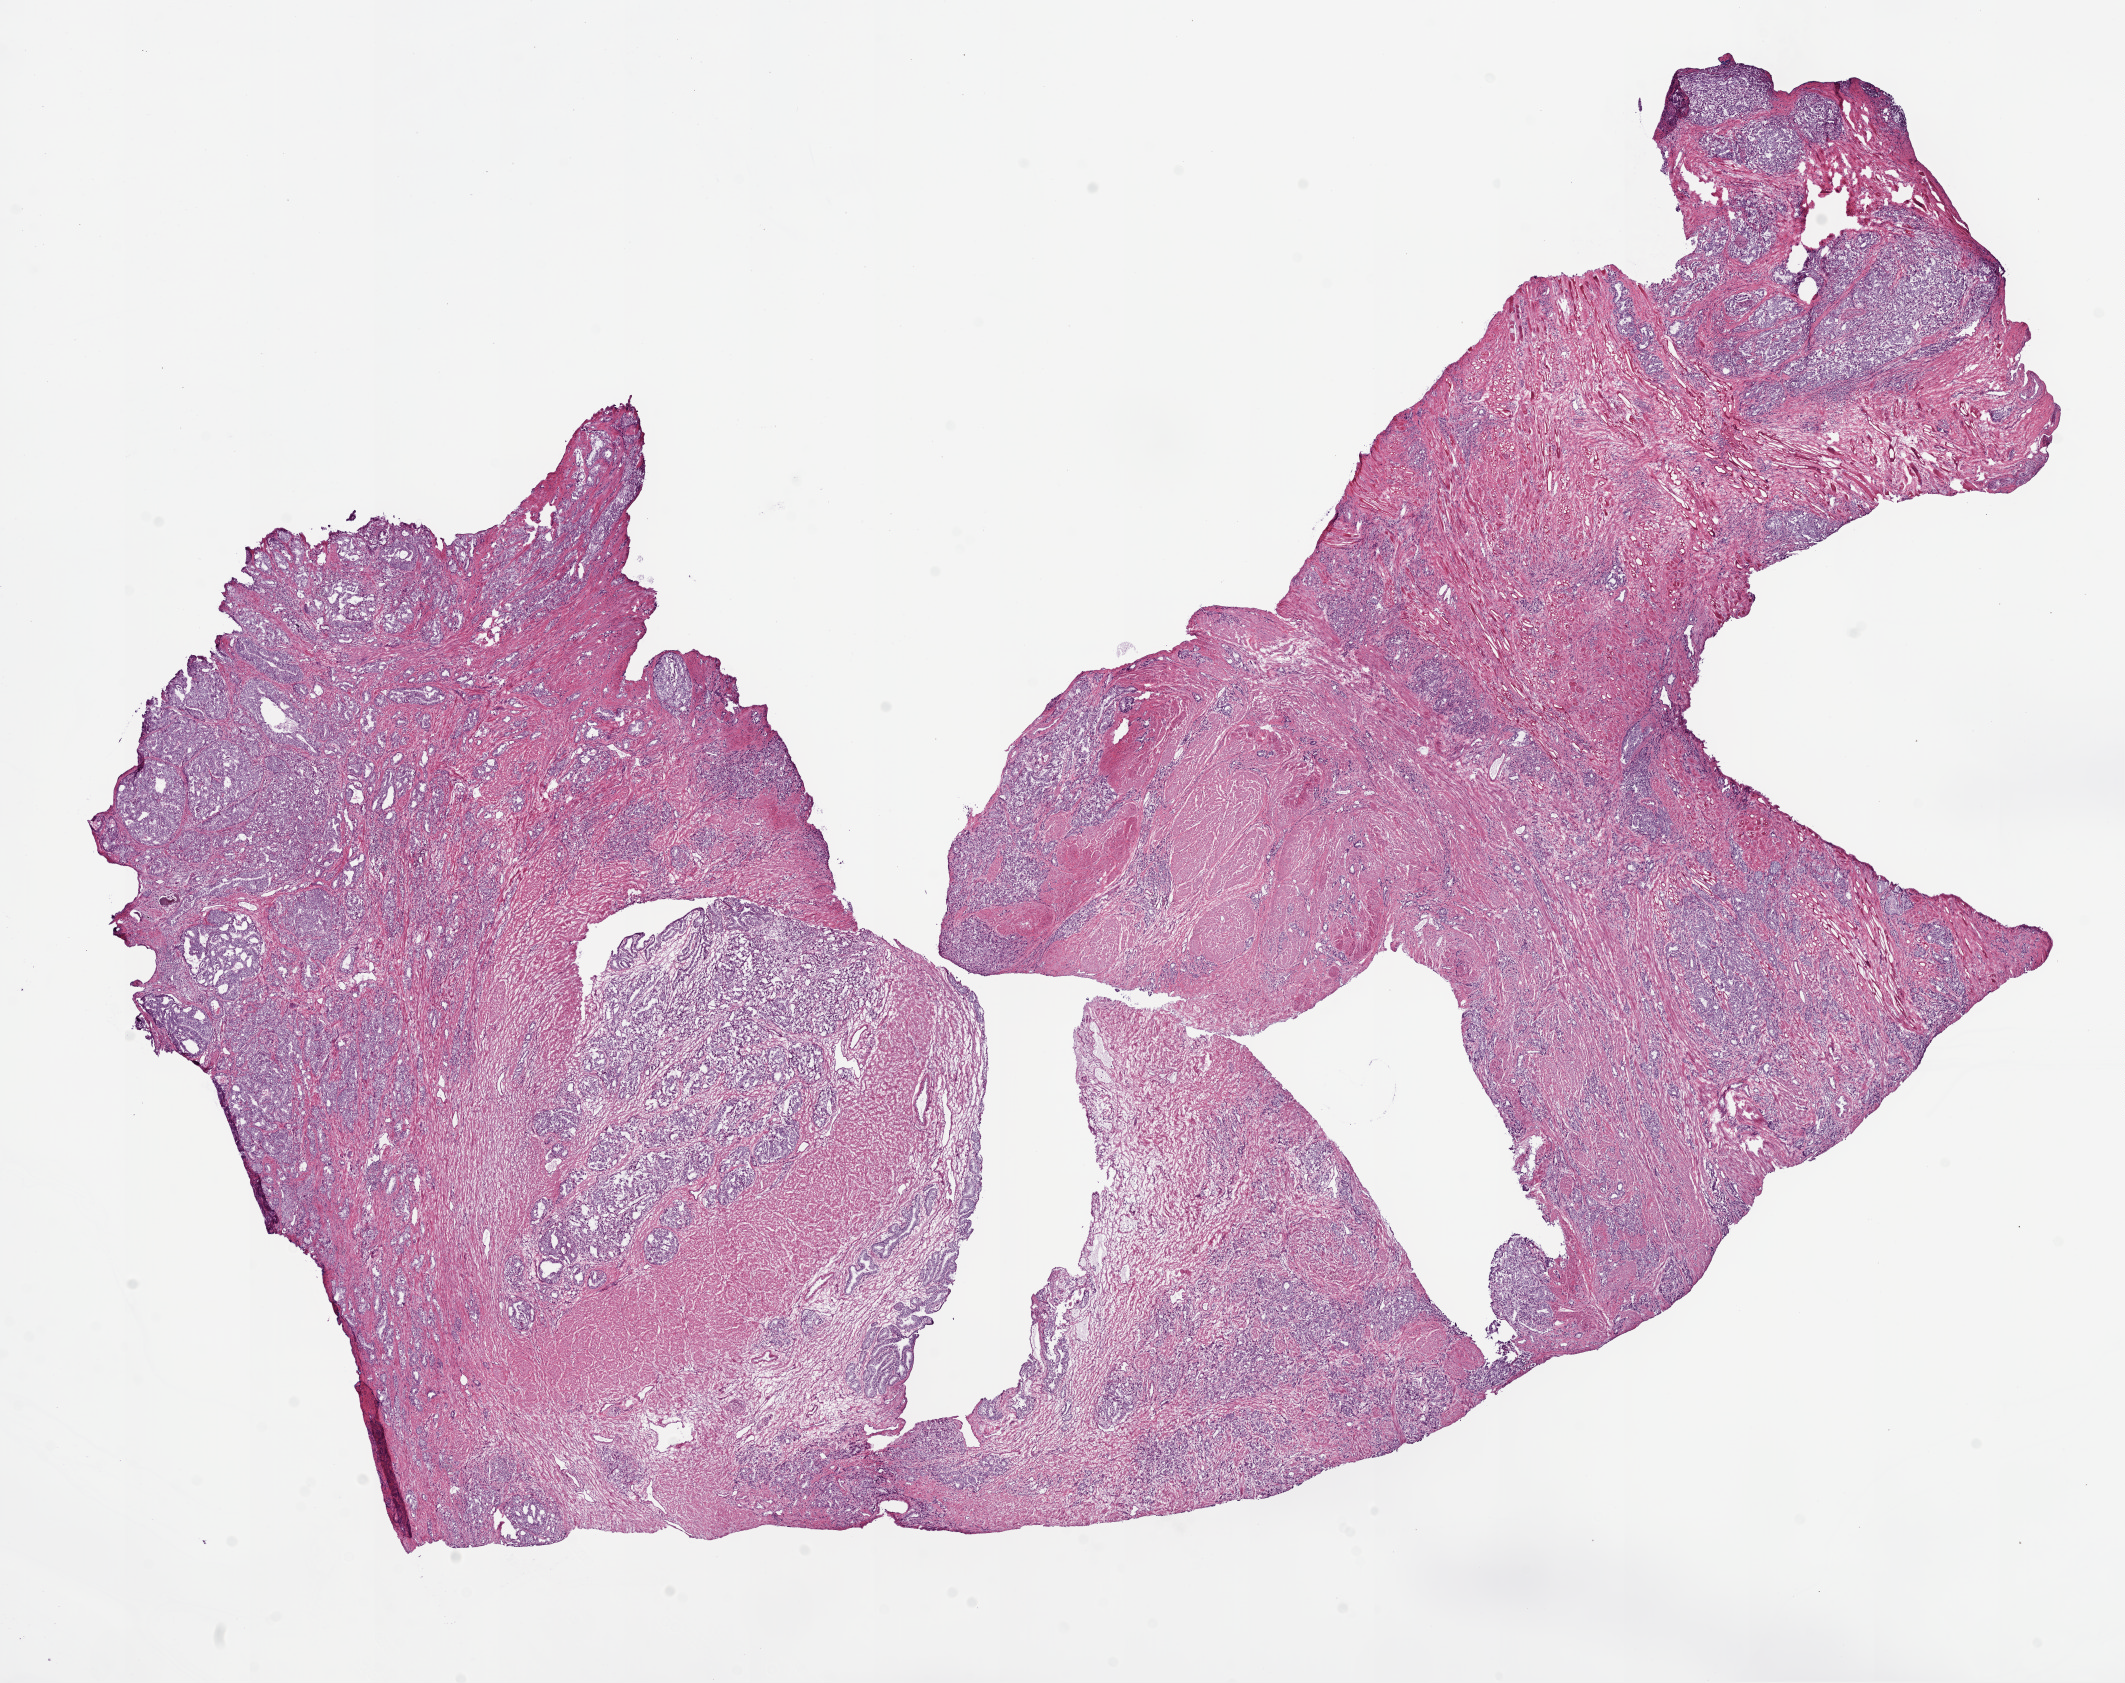
Digitized H&E tissue section (whole slide), shown as a low-resolution overview of the whole scanned area (about 17.1 x 13.5 mm, acquisition: 20x scan); frozen section from the top of the tissue portion; prostate, primary tumour sample. Male patient; age at initial diagnosis 66 years. Gleason score: 9 (4+5). Composition of this section per pathologist review: tumour cells 50%, tumour nuclei 55%, normal cells 20%, stromal cells 30%, necrosis 0%. Infiltration values recorded for this section: lymphocyte infiltration 0%, monocyte infiltration 0%, neutrophil infiltration 0%.
Lymph nodes positive (case pathology): 0 of 3 examined. Pathologic diagnosis: Acinar cell carcinoma (prostate gland).